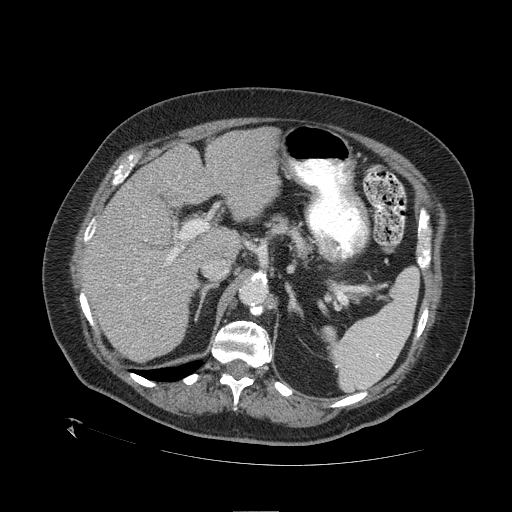
Contrast-enhanced abdominal CT (liver protocol), one axial slice; slice 70 of 109 in the series (ordered by position); reconstruction kernel STANDARD; 120 kVp; one of 2 acquisitions stored at this slice position; soft-tissue window (W 400 / L 40 HU); 2.5 mm slice thickness; 512 × 512 image matrix. From the clinical record (not read from this slice): diagnosis: hepatocellular carcinoma (patient treated with transarterial chemoembolisation; whether this scan precedes or follows treatment is not stated here); TNM stage (as recorded): Stage-I; Child-Pugh class: A; tumour differentiation: no biopsy; tumour nodularity: uninodular.
Outlined on this slice (semi-automatic segmentation, software-assisted and operator-edited):
- liver parenchyma outside the tumour (the mass and vessels are separate outlines, so this box may not span the whole liver): bounding box [x1, y1, x2, y2] px = [82, 126, 280, 362]
- liver vessels: [86, 220, 179, 280]